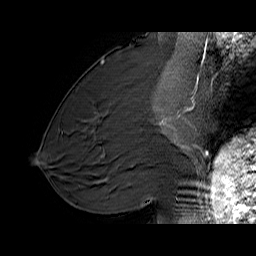
Breast MRI (dynamic contrast-enhanced), one sagittal slice. Position 28 of 60 along the scan axis. Dynamic contrast-enhanced series, time point 2 of 6 at this slice position (early post-contrast). 1.5 T. TE 6.1 ms, TR 32.9 ms. 4 mm slice thickness. 256 × 256 image matrix. Female patient. From the clinical record (not read from this slice): setting: breast cancer imaged before/during neoadjuvant chemotherapy; receptor status: HER2-positive.
Annotated regions visible in this slice (semi-automatically segmented with operator editing):
- analysis volume of interest (the breast-tissue region the enhancement analysis was run in; not a lesion): bounding box (x1, y1, x2, y2) in pixels: (127, 95, 194, 165)
- tumour enhancement mask (voxels above the 100 % enhancement threshold inside the analysis volume of interest): (161, 102, 194, 148)